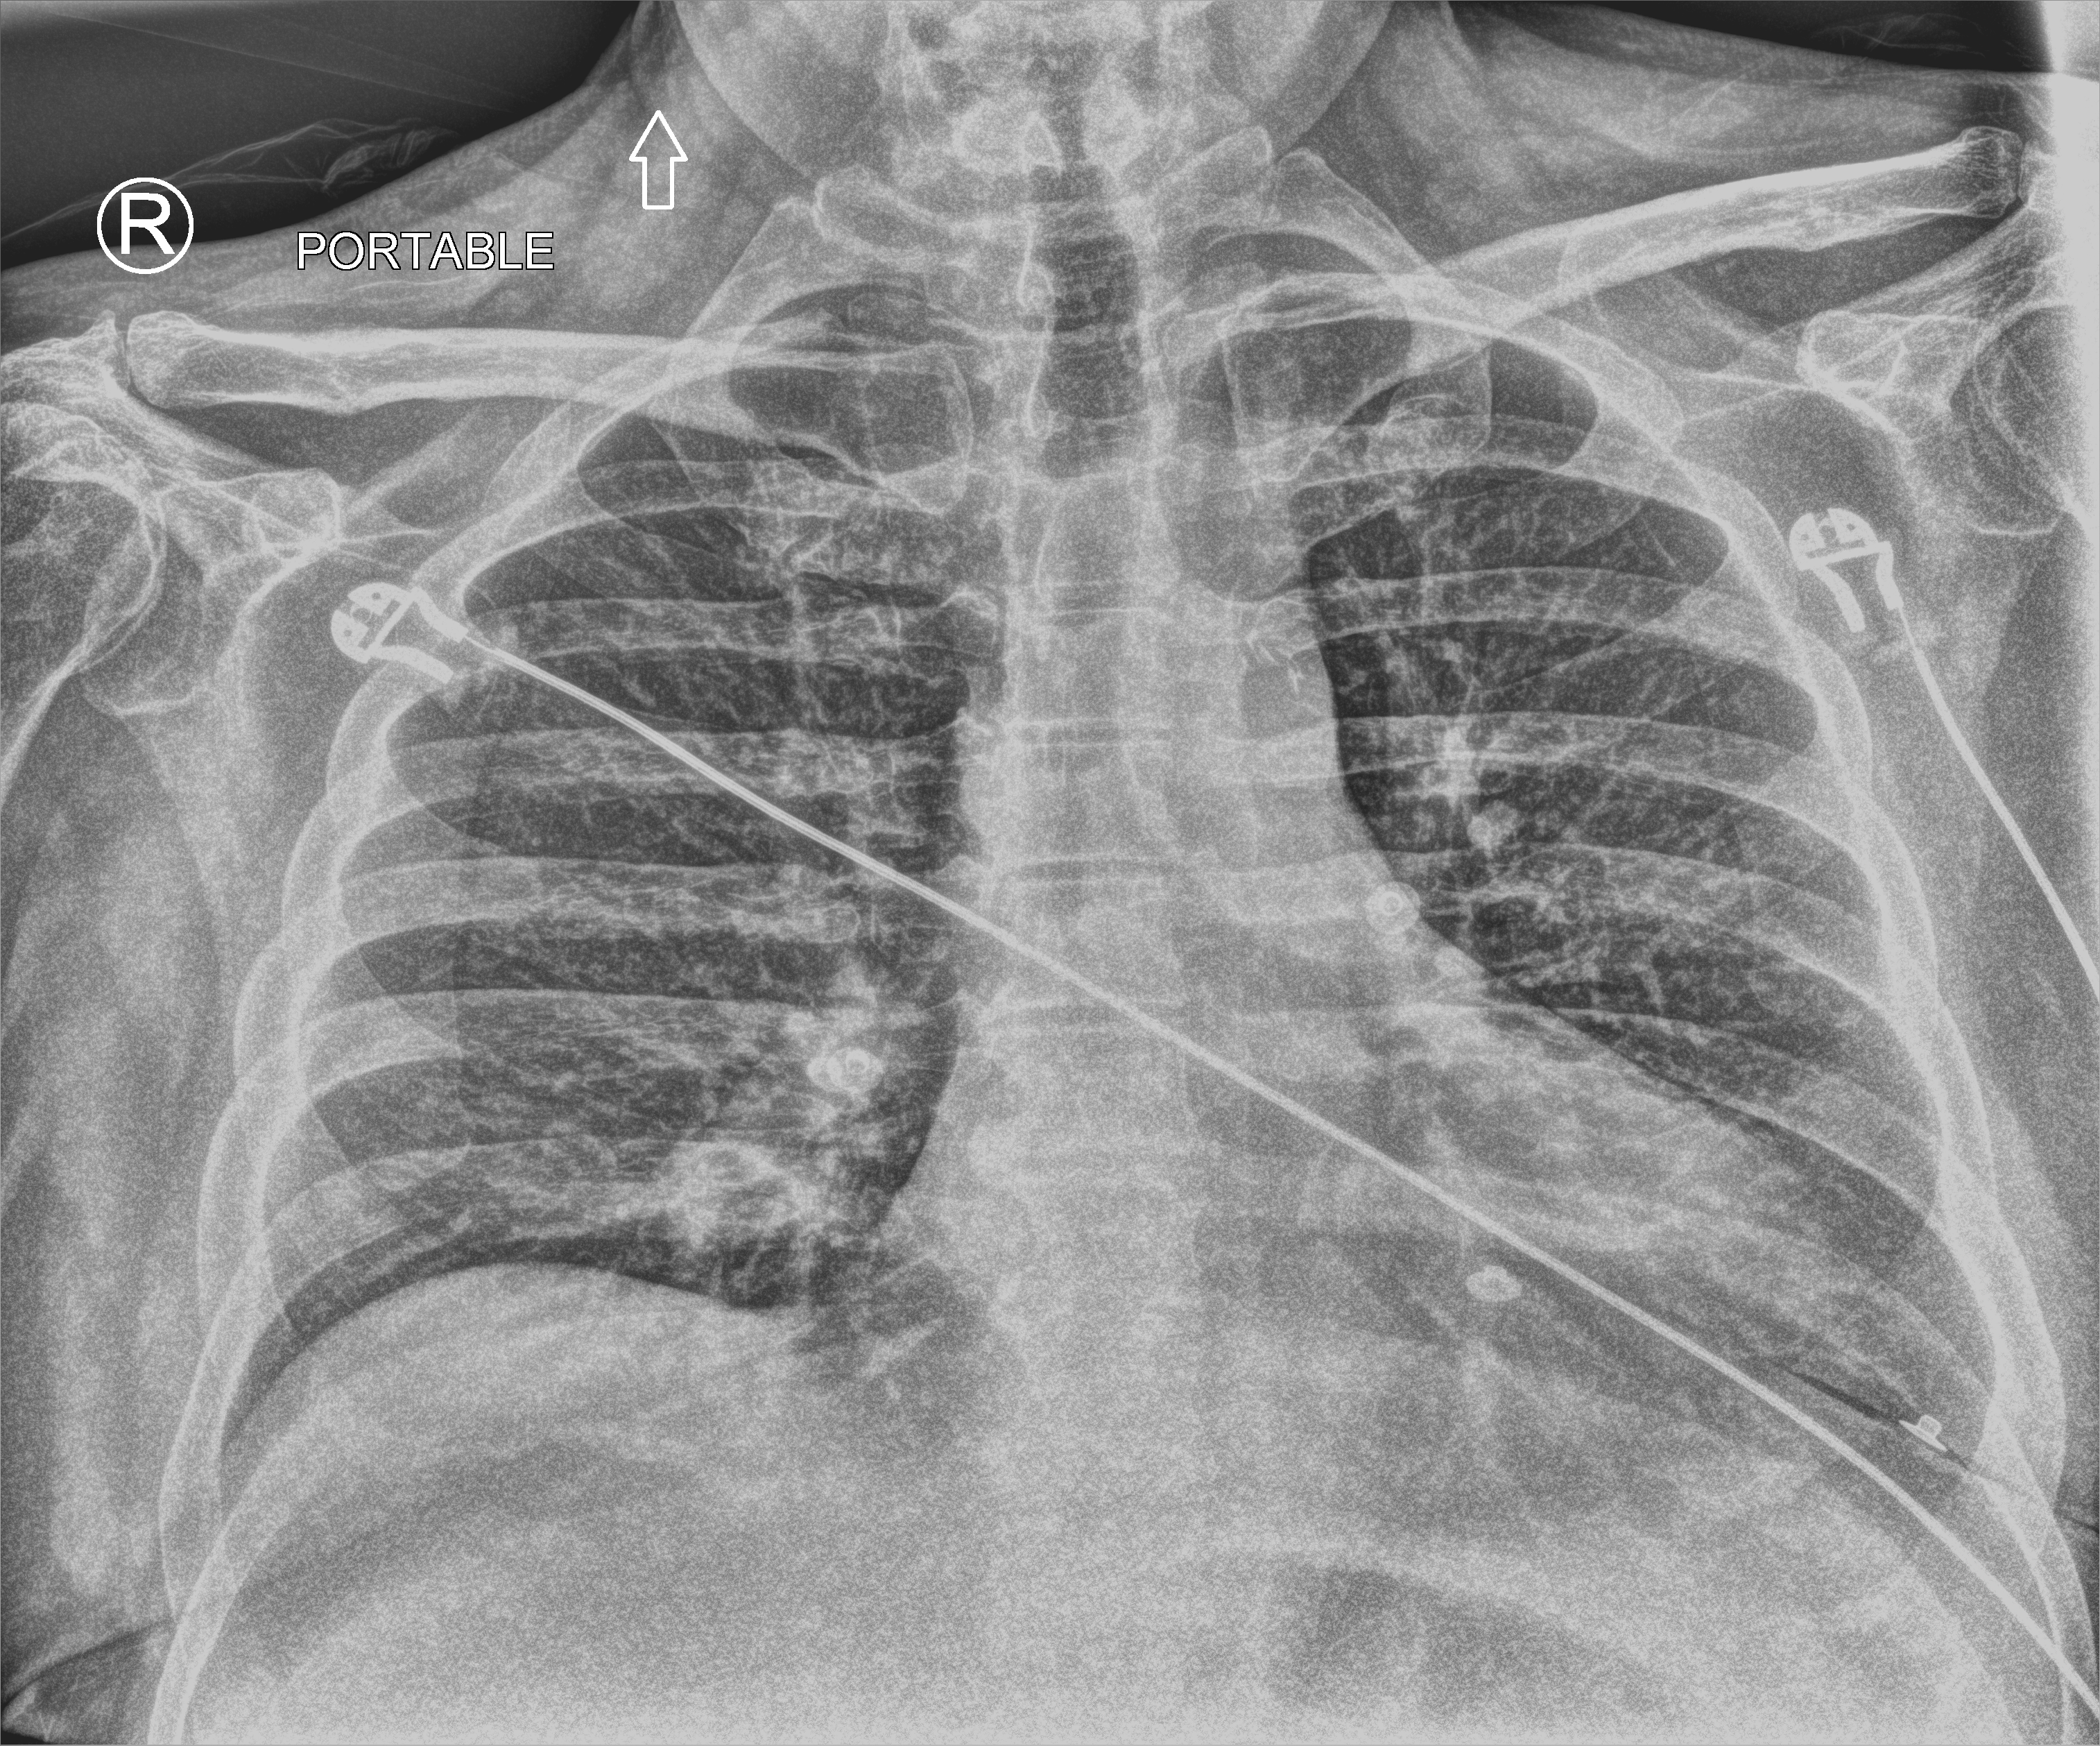
Chest X-ray (portable), anteroposterior (AP) projection. Male patient hospitalised with COVID-19, age 60–74 years.
Admission-level facts for this patient (not findings on this image; timing relative to this image not recorded): mechanically ventilated during this hospital stay: no.